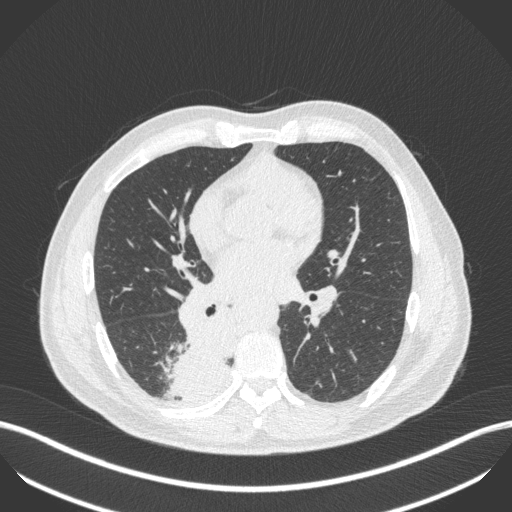
Chest CT, one axial slice. Slice 232 of 451 in the series (ordered by position). Reconstruction kernel B31f. Lung window (W 1500 / L -600 HU). 512 × 512 image matrix, field of view 400 × 400 mm. Patient: male, 61 years. Case-level facts recorded for this patient, not image findings: clinical TNM (as recorded): T1 N0 M0.
Outlined on this slice (rectangle marked by the reading radiologist):
- lung tumour (recorded histology: small cell carcinoma): bounding box (x1, y1, x2, y2) in pixels: (159, 312, 237, 398)